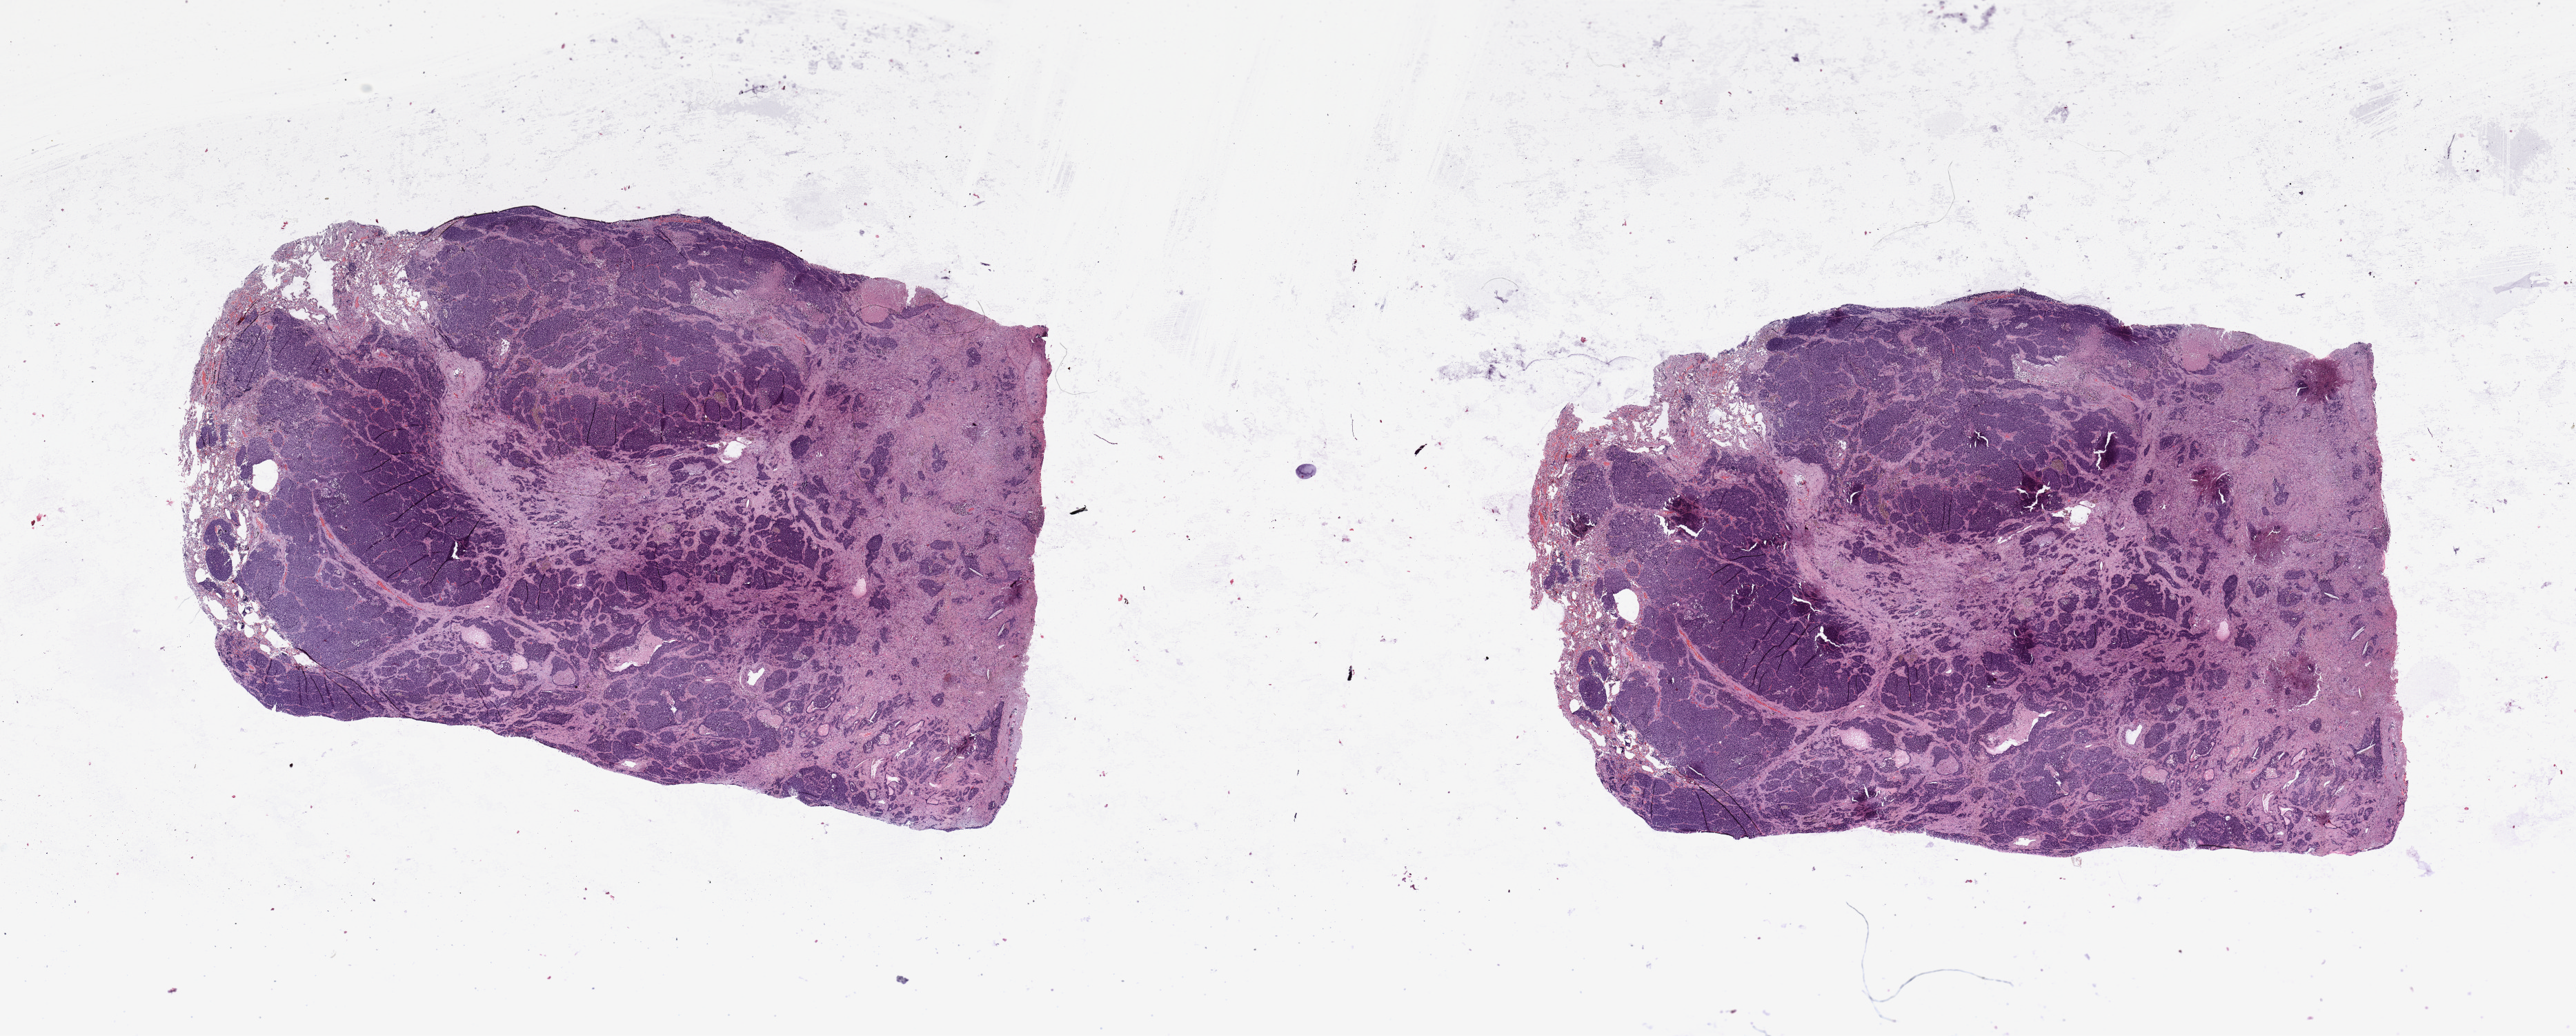
Digitized H&E-stained tissue section (whole slide) — a low-resolution overview of the entire scanned area, about 29.5 x 11.9 mm (from a 20x scan), tumour tissue sample, lung. Male, 63 y/o.
• patient diagnosis (cohort enrolment): squamous cell carcinoma (lung)
• primary tumour site (as recorded): left upper lobe